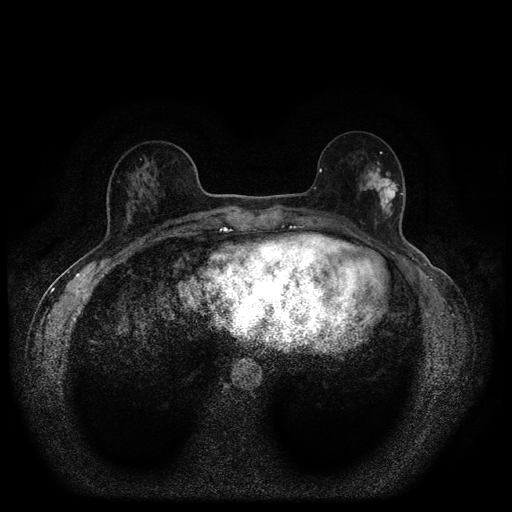
Breast MRI (dynamic contrast-enhanced, multi-phase), one axial slice. Slice 38 of 116 in the series (ordered by position). Dynamic contrast-enhanced series, time point 2 of 5 at this slice position (early post-contrast). 1.5 T. TE 2.7 ms, TR 5.4 ms. 2 mm slice thickness. 512 × 512 image matrix. Female patient, age 56 years.
Structures marked on this image (semi-automatic segmentation, software-assisted and operator-edited):
- breast lesion (labelled 'tumour' in the annotation; benign lesions carry a separate 'benign' label): bounding box (x1, y1, x2, y2) in pixels: (357, 155, 401, 225)